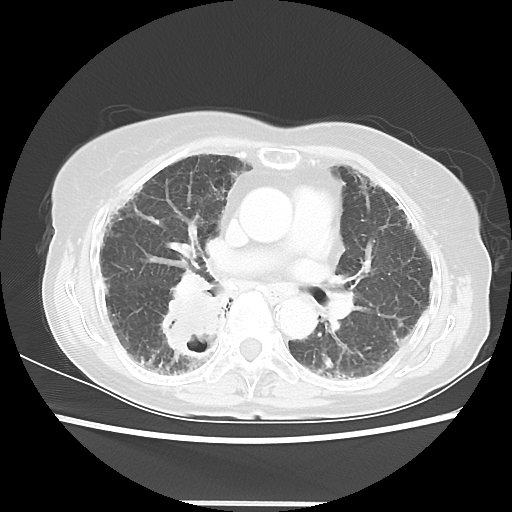
Chest CT, one axial slice. Position 29 of 52 along the scan axis. Reconstruction kernel LUNG. Lung window (W 1500 / L -600 HU). 512 × 512 image matrix, field of view 325 × 325 mm. Female patient, age 71 years. From the clinical record (not read from this slice): clinical TNM (as recorded): T3 N0 M0.
Annotated regions visible in this slice (bounding box drawn by a radiologist):
- lung tumour (recorded histology: squamous cell carcinoma): box from (x=154, y=279) to (x=231, y=364) px